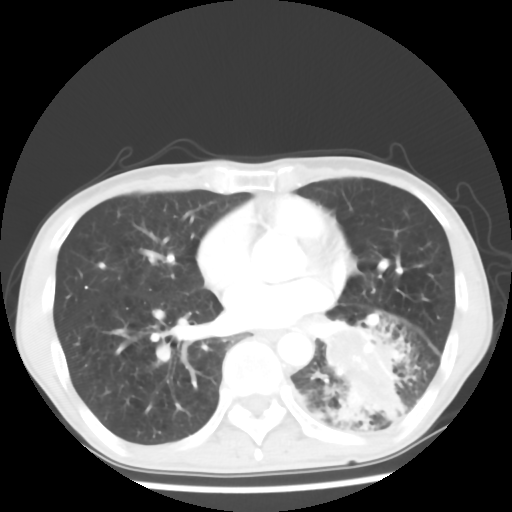
Chest CT, one axial slice. Slice 27 of 64 in the series (ordered by position). 120 kVp. Lung window (W 1500 / L -600 HU). 512 × 512 image matrix. Male patient, age 68 years. Case-level facts recorded for this patient, not image findings: clinical TNM (as recorded): T4 N0 M0.
Outlined on this slice (bounding box drawn by a radiologist):
- lung tumour (recorded histology: squamous cell carcinoma): bounding box <320,309,380,386> (left, top, right, bottom; pixels)